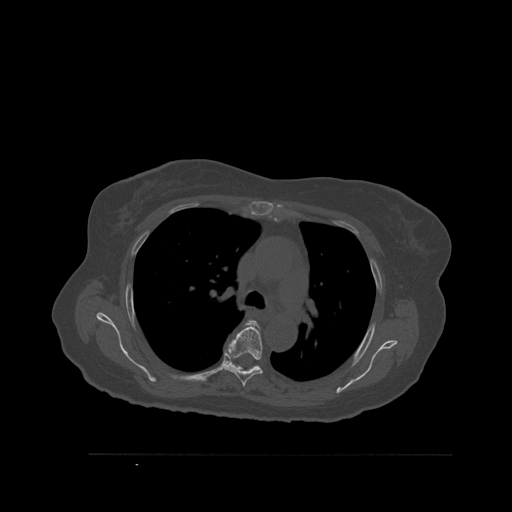
CT including the spine, one axial slice; slice 393 of 527 in the series (ordered by position); bone window (W 1800 / L 400 HU); 512 × 512 image matrix, field of view 470 × 470 mm. Patient: female, 73 years. Case-level facts recorded for this patient, not image findings: primary cancer: breast; vertebrae with lytic lesions (as recorded): L2.
Outlined on this slice (semi-automatic segmentation, software-assisted and operator-edited):
- T4 vertebra: bounding box (x1, y1, x2, y2) in pixels: (249, 321, 256, 324)
- T5 vertebra: (223, 322, 262, 387)
- T6 vertebra: (227, 363, 261, 371)